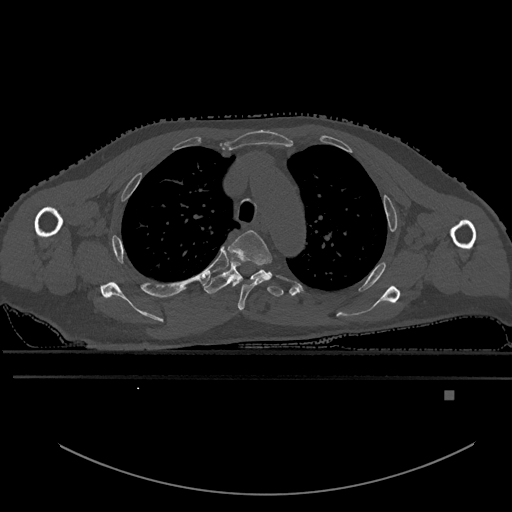
CT including the spine, one axial slice. Position 429 of 969 along the scan axis. Bone window (W 1800 / L 400 HU). 0.5 mm slice thickness. 512 × 512 image matrix. Patient: male, 82 years. Case-level facts recorded for this patient, not image findings: primary cancer: prostate; vertebrae with lytic lesions (as recorded): T11, T9, T8, T2.
Structures marked on this image (semi-automatically segmented with operator editing):
- T3 vertebra: box from (x=228, y=230) to (x=273, y=311) px
- T4 vertebra: (x=203, y=262)–(x=284, y=297)